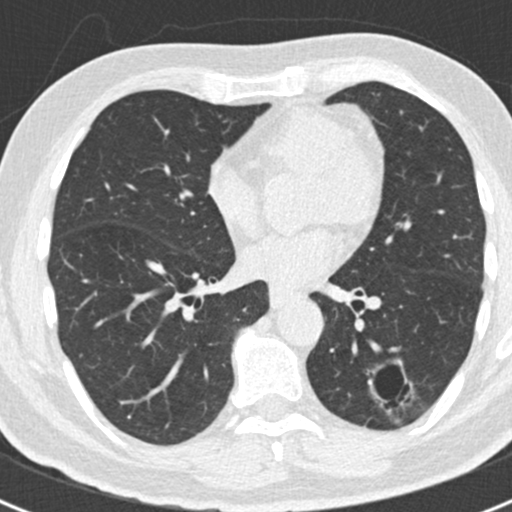
Axial slice from a low-dose chest CT screening exam, first (baseline) screen, lung window (W 1500 / L -600 HU), slice 94 of 188 in the series, 512 × 512 image matrix. Male, age 66 years at enrolment.
• Expert-annotated lung lesion, bounding box [x1, y1, x2, y2] px = [346, 341, 421, 420].
• Reader record for this screening exam (exam-level; its link to the box is not recorded): non-calcified nodule or mass ≥4 mm, left lower lobe, 43 × 27 mm, smooth margins.
• Official screen result: positive, change unspecified: nodule(s) >= 4 mm or enlarging nodule(s), mass(es), or other non-specific abnormalities suspicious for lung cancer.
• Lung cancer was diagnosed 801 days after this screen: adenocarcinoma, NOS, left lower lobe, poorly differentiated (G3), stage IB (AJCC 6th edition), 38 mm at pathology.